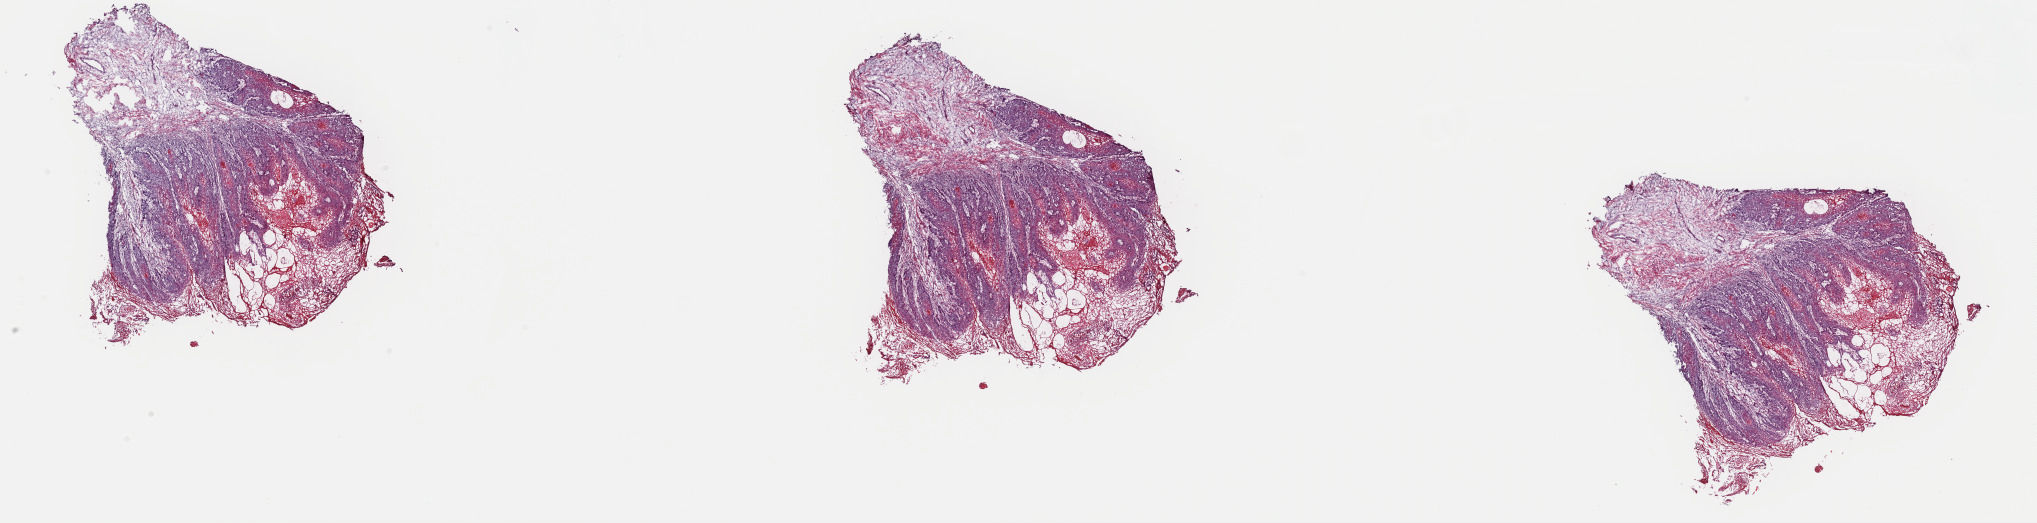
Digitized H&E tissue section (whole slide) — shown as a low-resolution overview of the whole scanned area (about 32.2 x 8.3 mm), frozen section from the top of the tissue portion, head and neck, primary tumour sample. Male, age 56 years at initial diagnosis. Histologic grade: G1 (well differentiated). Composition of this section per pathologist review: tumour cells 75%, tumour nuclei 75%, normal cells 10%, stromal cells 15%, necrosis 0%. Inflammatory infiltration, as recorded: lymphocyte infiltration 5%, monocyte infiltration 0%, neutrophil infiltration 0%.
Laterality: left. AJCC pathologic stage: IVA (7th edition). Pathologic diagnosis: Squamous cell carcinoma, keratinizing, NOS.